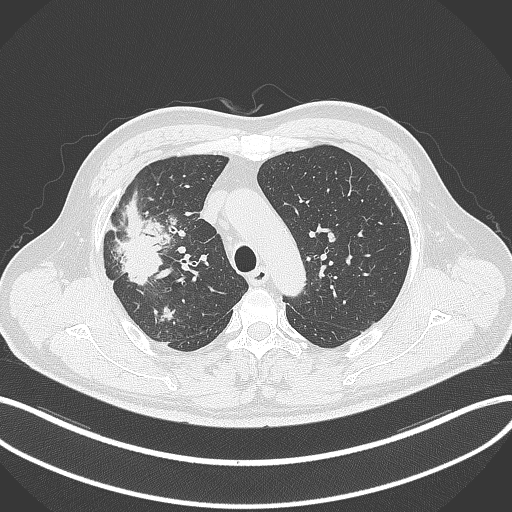
Chest CT, one axial slice; position 250 of 348 along the scan axis; reconstruction kernel B70f; 120 kVp; lung window (W 1500 / L -600 HU); 512 × 512 image matrix, field of view 400 × 400 mm. Patient: male, 55 years. From the clinical record (not read from this slice): clinical TNM (as recorded): T3 N2 M1.
Outlined on this slice (rectangle marked by the reading radiologist):
- lung tumour (recorded histology: adenocarcinoma): bounding box [x1, y1, x2, y2] px = [113, 189, 164, 288]